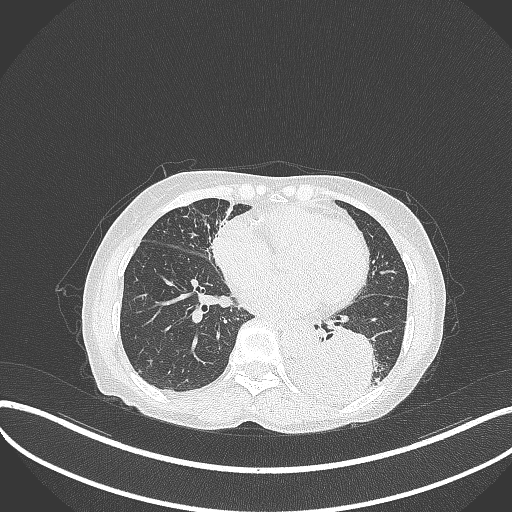
Chest CT, one axial slice; slice 115 of 370 in the series (ordered by position); 120 kVp; lung window (W 1500 / L -600 HU); 512 × 512 image matrix, field of view 400 × 400 mm. Female patient, age 78 years. Case-level facts recorded for this patient, not image findings: clinical TNM (as recorded): T3 N0 M1.
Structures marked on this image (bounding box drawn by a radiologist):
- lung tumour (recorded histology: squamous cell carcinoma): bounding box <281,324,376,406> (left, top, right, bottom; pixels)